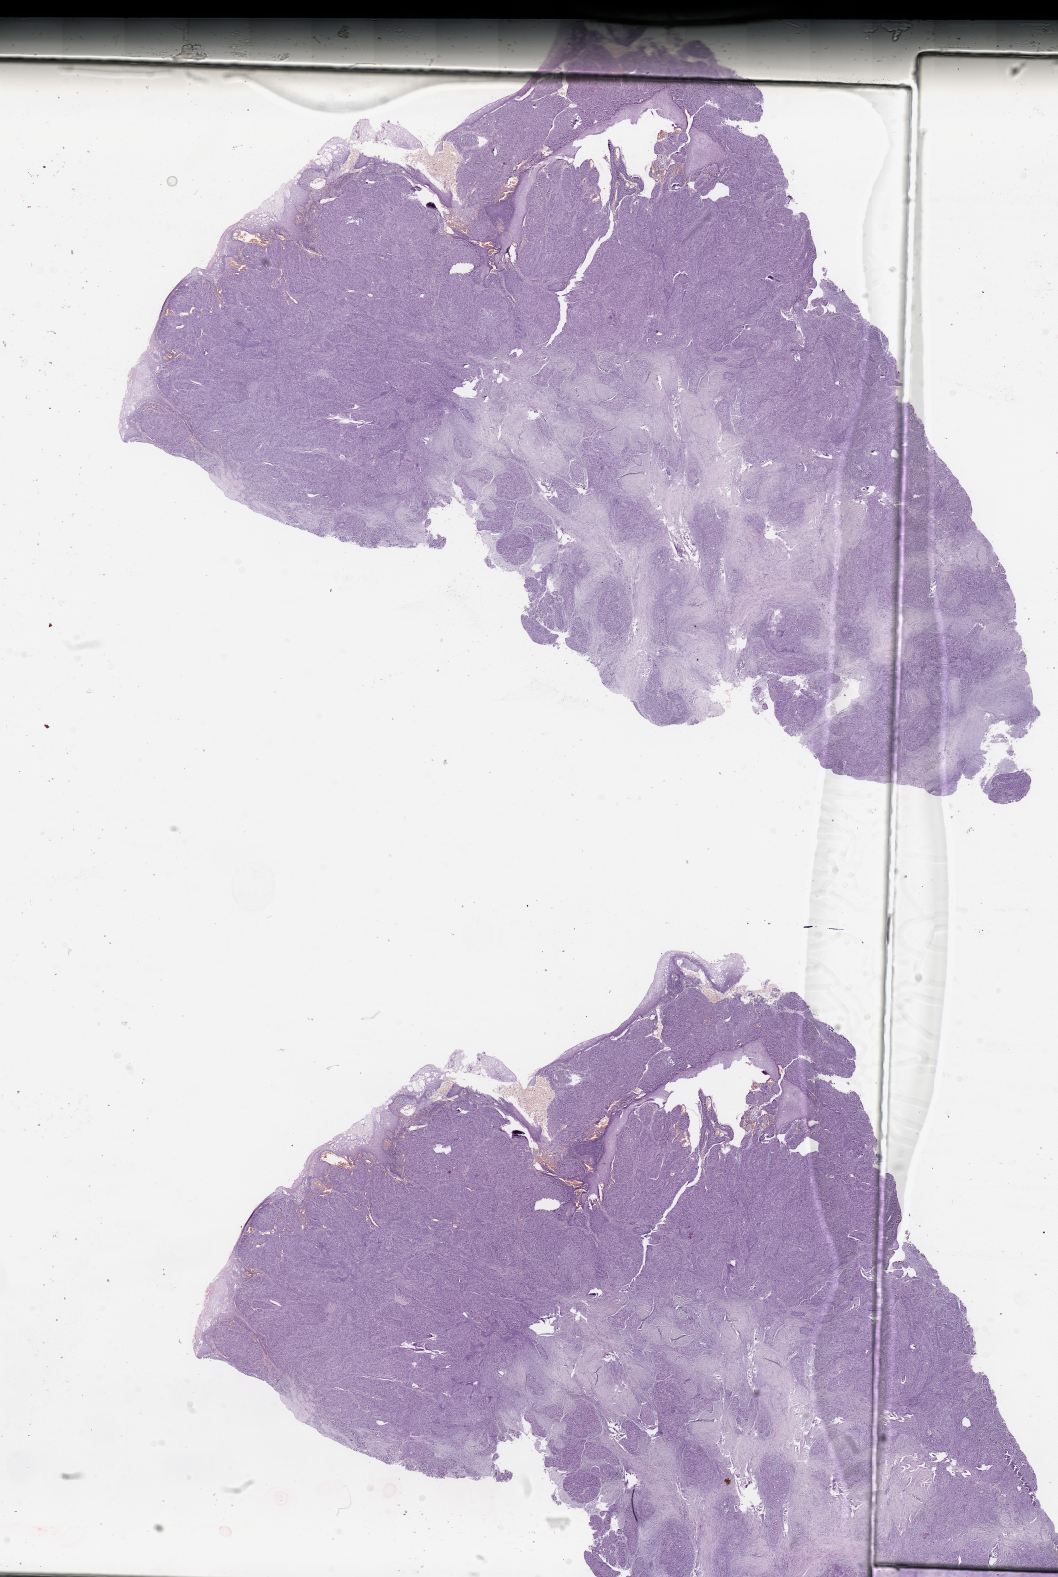
Whole-slide histology image, H&E, shown as a low-resolution overview of the whole scanned area (about 16.7 x 24.9 mm, slide scanned at 20x), head and neck, tissue type not recorded. 64-year-old male patient.
- patient diagnosis: Squamous cell carcinoma, NOS (base of tongue, NOS)